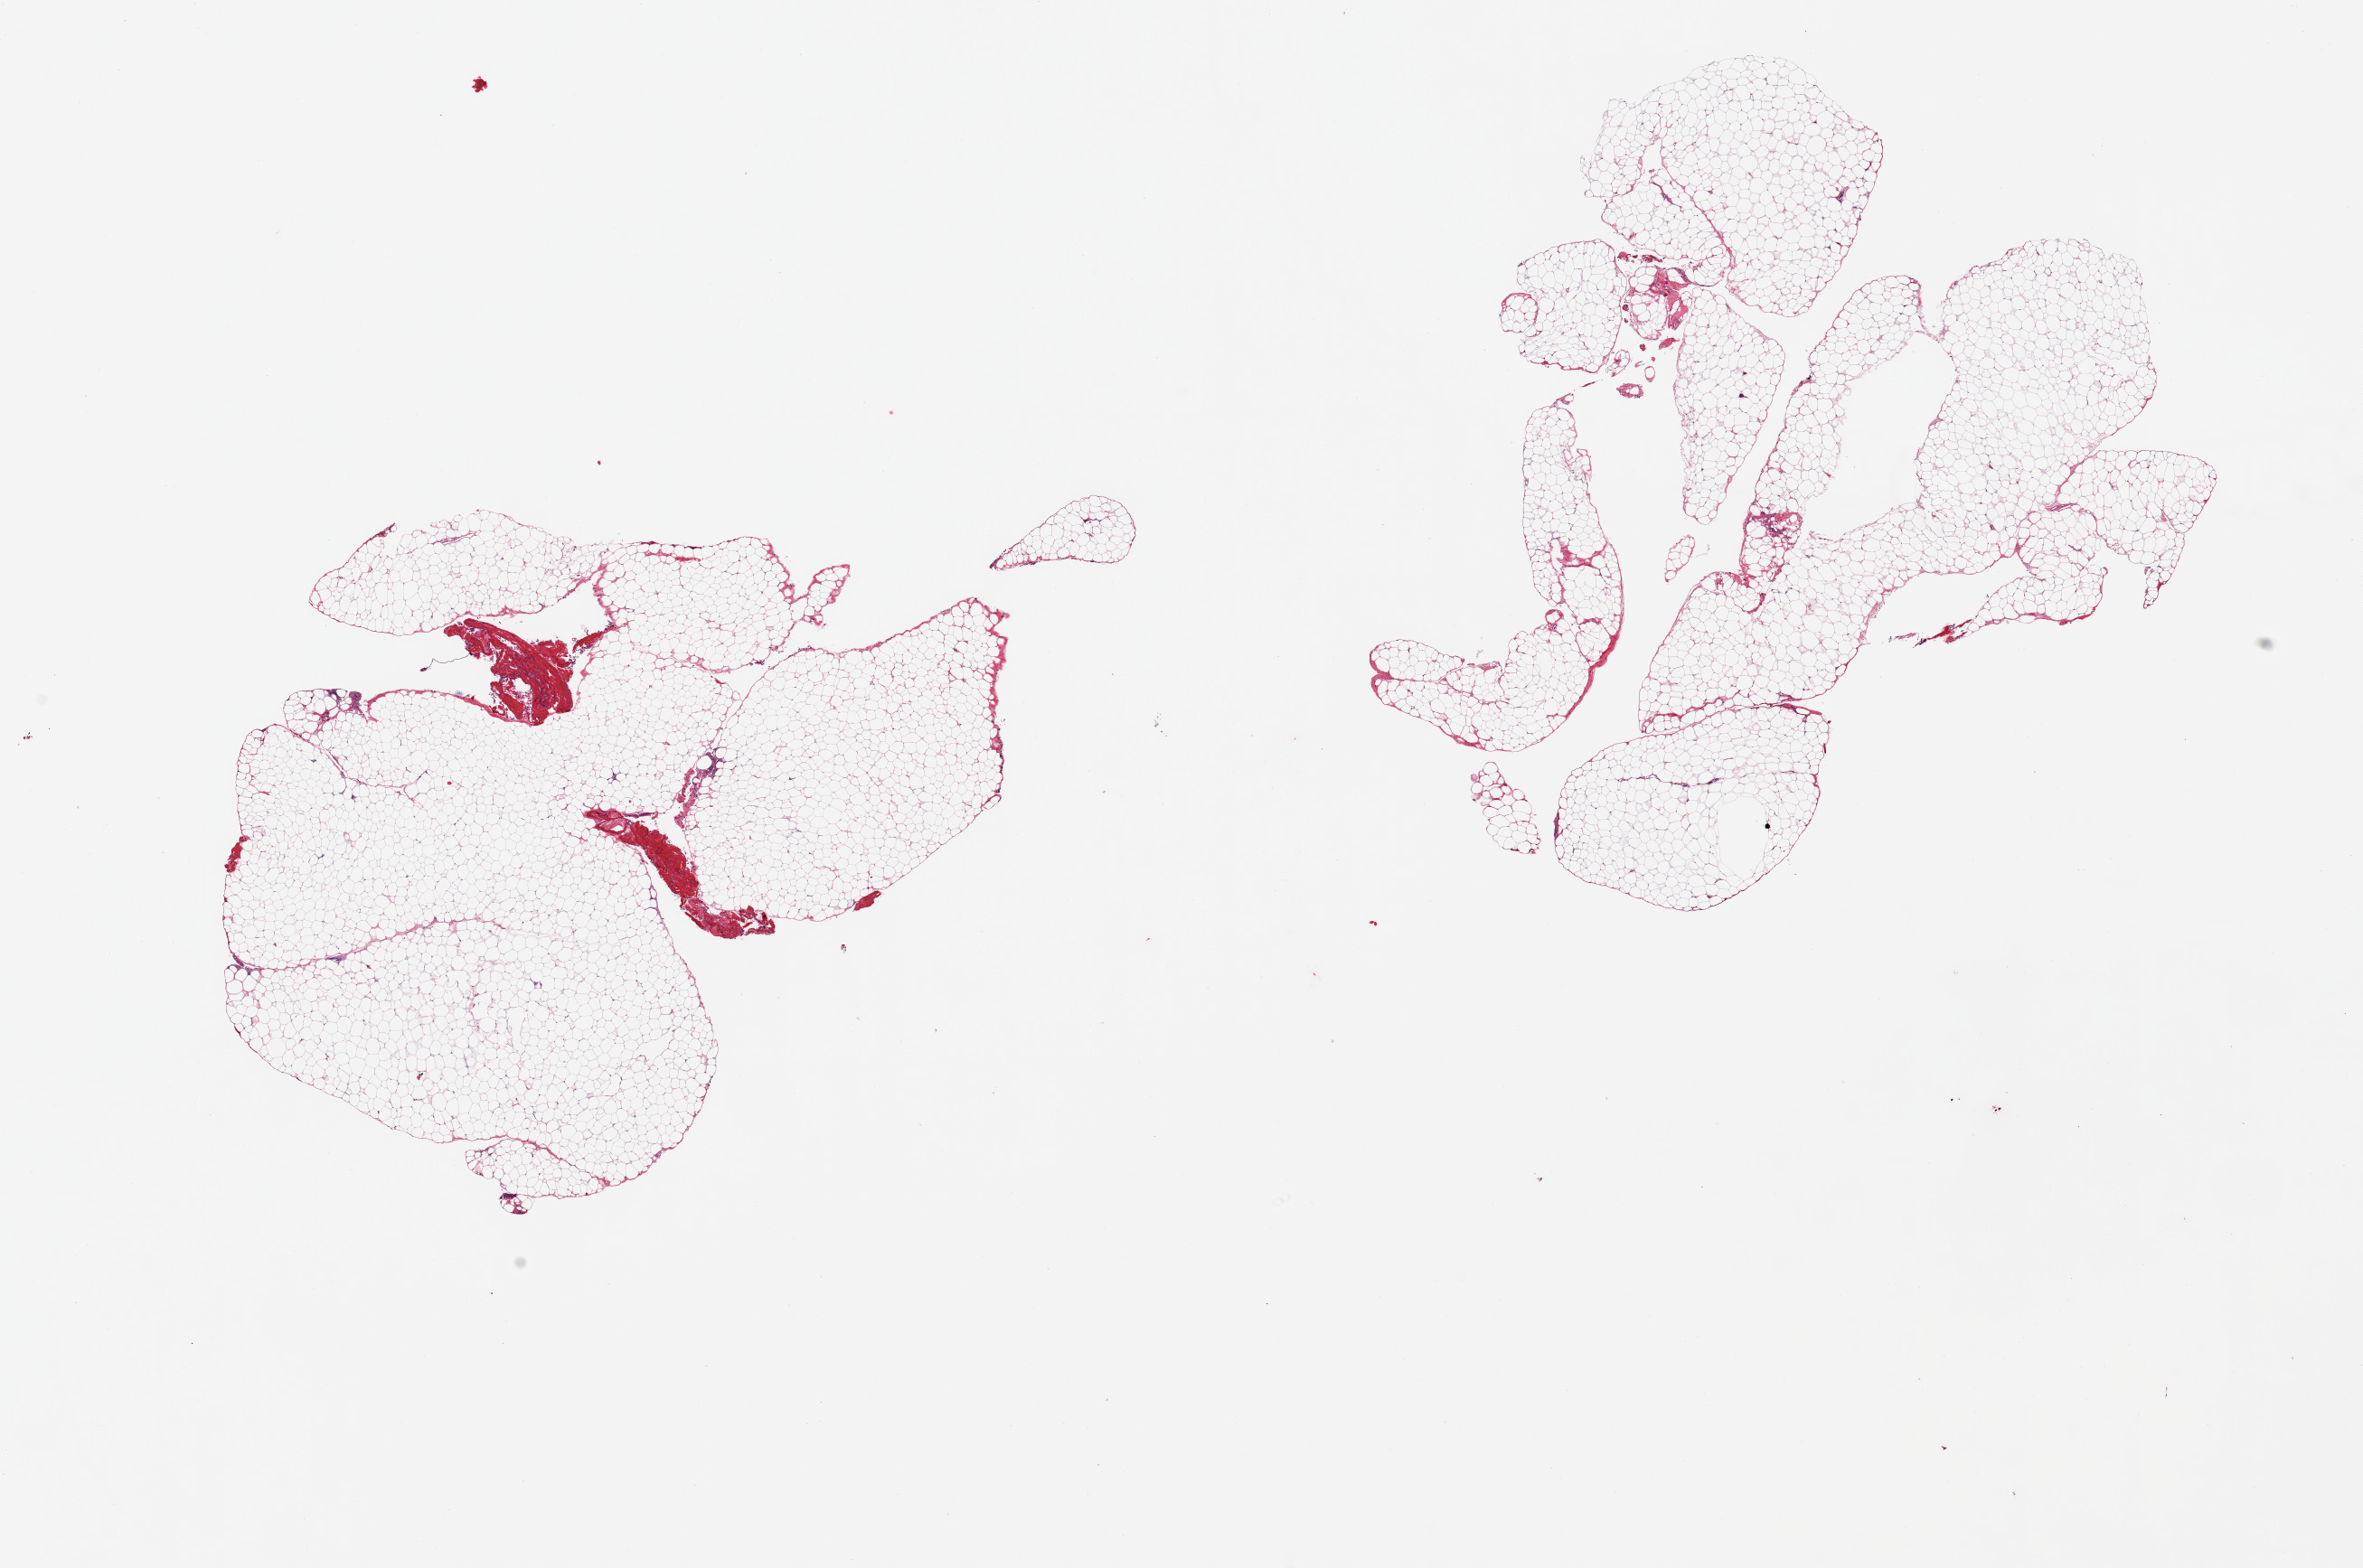
Whole-slide image, haematoxylin and eosin stain, whole scanned area (about 20.7 x 13.7 mm) shown as a low-resolution overview. PAXgene-fixed, paraffin-embedded tissue. Sampled site (target tissue): omentum. Tissue donor sample. Donor: male.
Pathologist's review note for this sample: 2 pieces; 5% fibrous content in 1 piece.